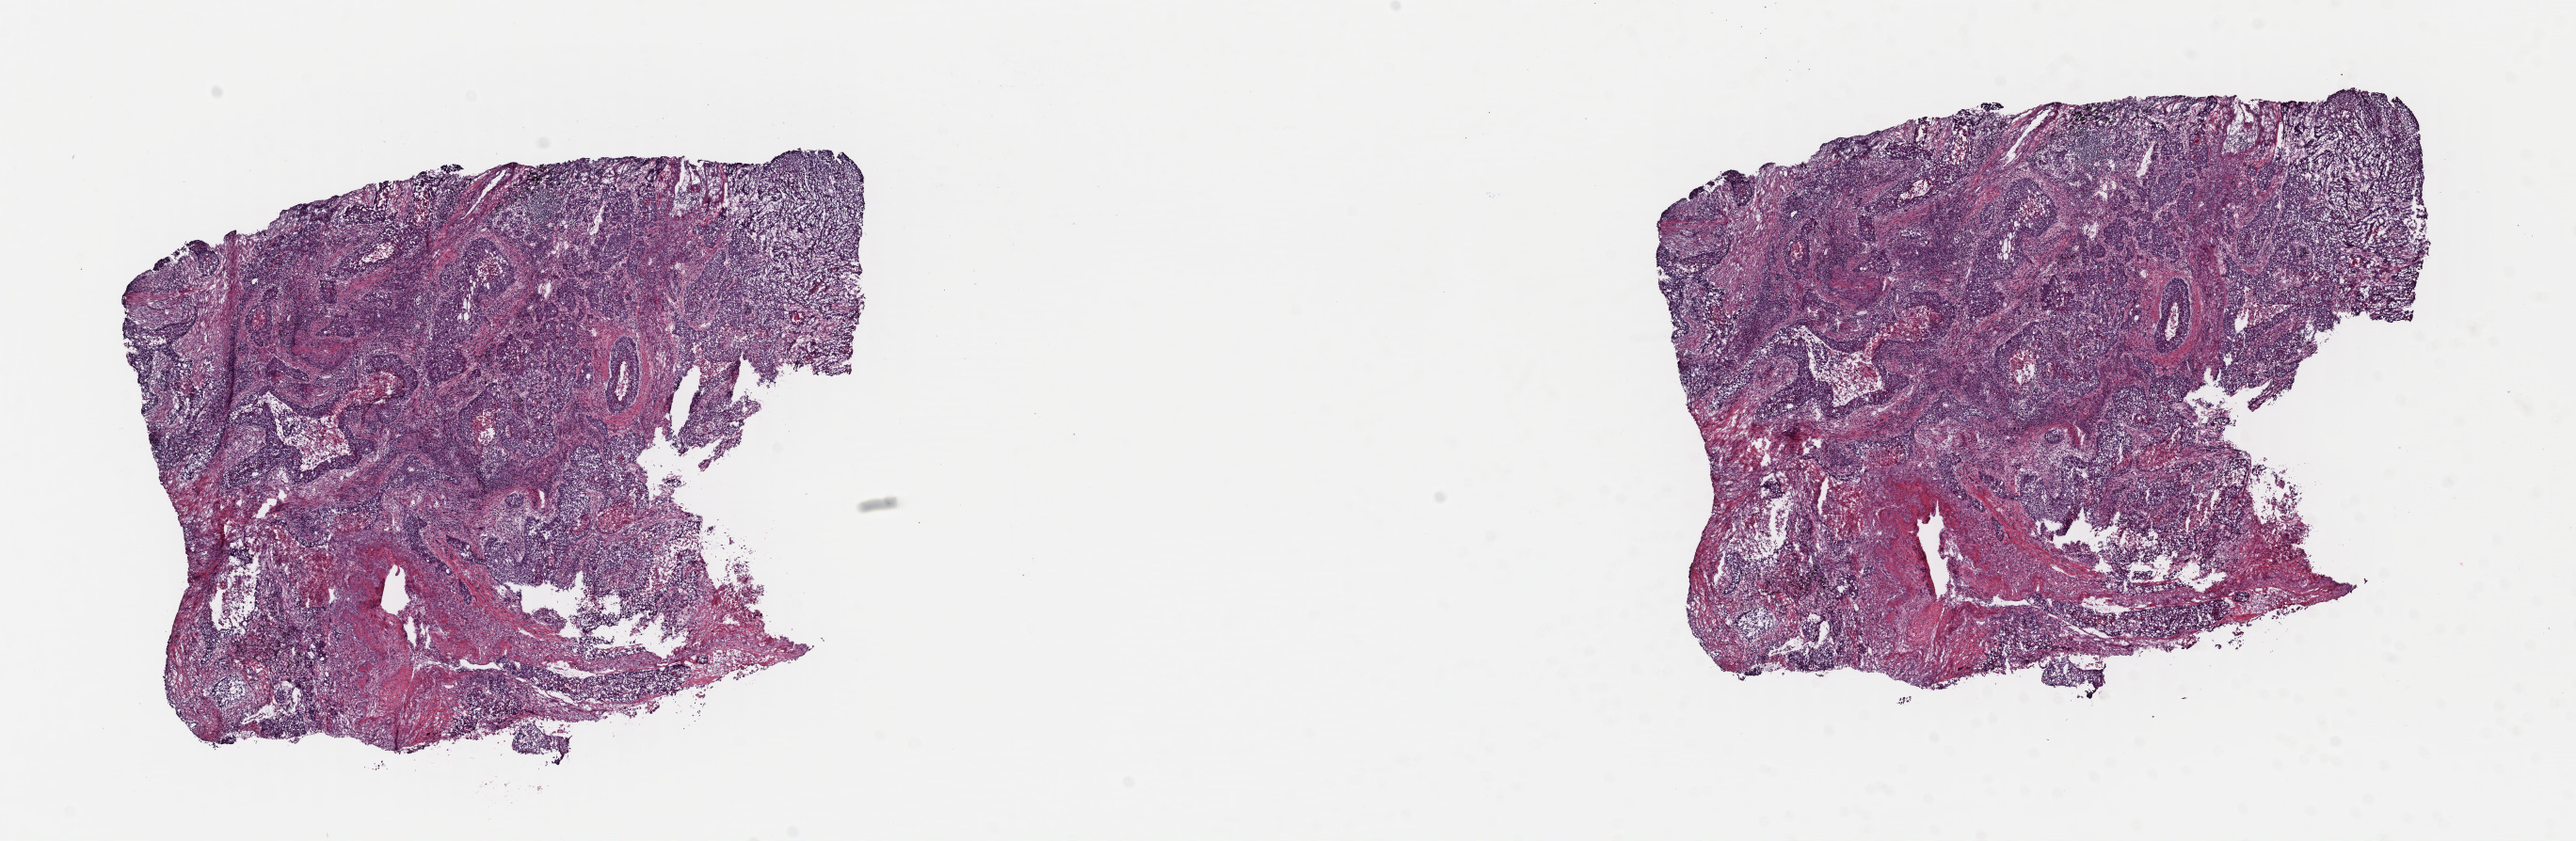
Whole-slide histology image, H&E — whole scanned area (about 21.5 x 7.0 mm, slide scanned at 40x) shown as a low-resolution overview. Frozen section from the top of the tissue portion. Lung, primary tumour sample. Male patient; age at initial diagnosis 70 years. Pathologist review of this section (percent, as recorded): tumour cells 85%, tumour nuclei 65%, normal cells 5%, stromal cells 0%, necrosis 10%. Infiltration values recorded for this section: lymphocyte infiltration 0%, monocyte infiltration 0%, neutrophil infiltration 0%.
TNM: T2a N1 M0. AJCC pathologic stage: IIA. Pathologic diagnosis: Squamous cell carcinoma, NOS.